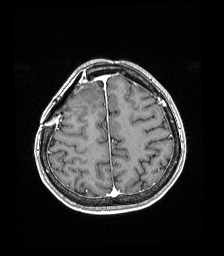
Brain MRI from a brain-tumour surgery series, one axial slice. Position 55 of 192 along the scan axis. T1-weighted post-contrast. 1 mm slice thickness. 224 × 256 image matrix. From the clinical record (not read from this slice): histopathology: Astrocytoma; WHO grade: 4; IDH mutation: yes; tumour location: Right superficial frontal.
Structures marked on this image (manually delineated by an expert):
- tumour: box from (x=79, y=91) to (x=85, y=96) px